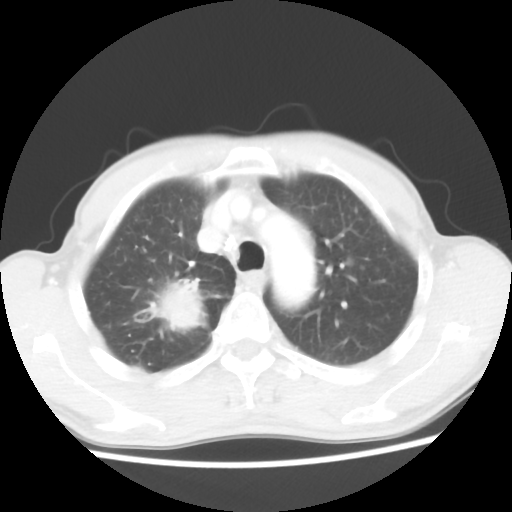
Chest CT, one axial slice; slice 41 of 52 in the series (ordered by position); reconstruction kernel STANDARD; 100 kVp; lung window (W 1500 / L -600 HU); 5 mm slice thickness; 512 × 512 image matrix. Patient: male, 66 years. From the clinical record (not read from this slice): clinical TNM (as recorded): T2 N0 M1a.
Structures marked on this image (rectangle marked by the reading radiologist):
- lung tumour (recorded histology: adenocarcinoma): bounding box (x1, y1, x2, y2) in pixels: (136, 270, 218, 333)